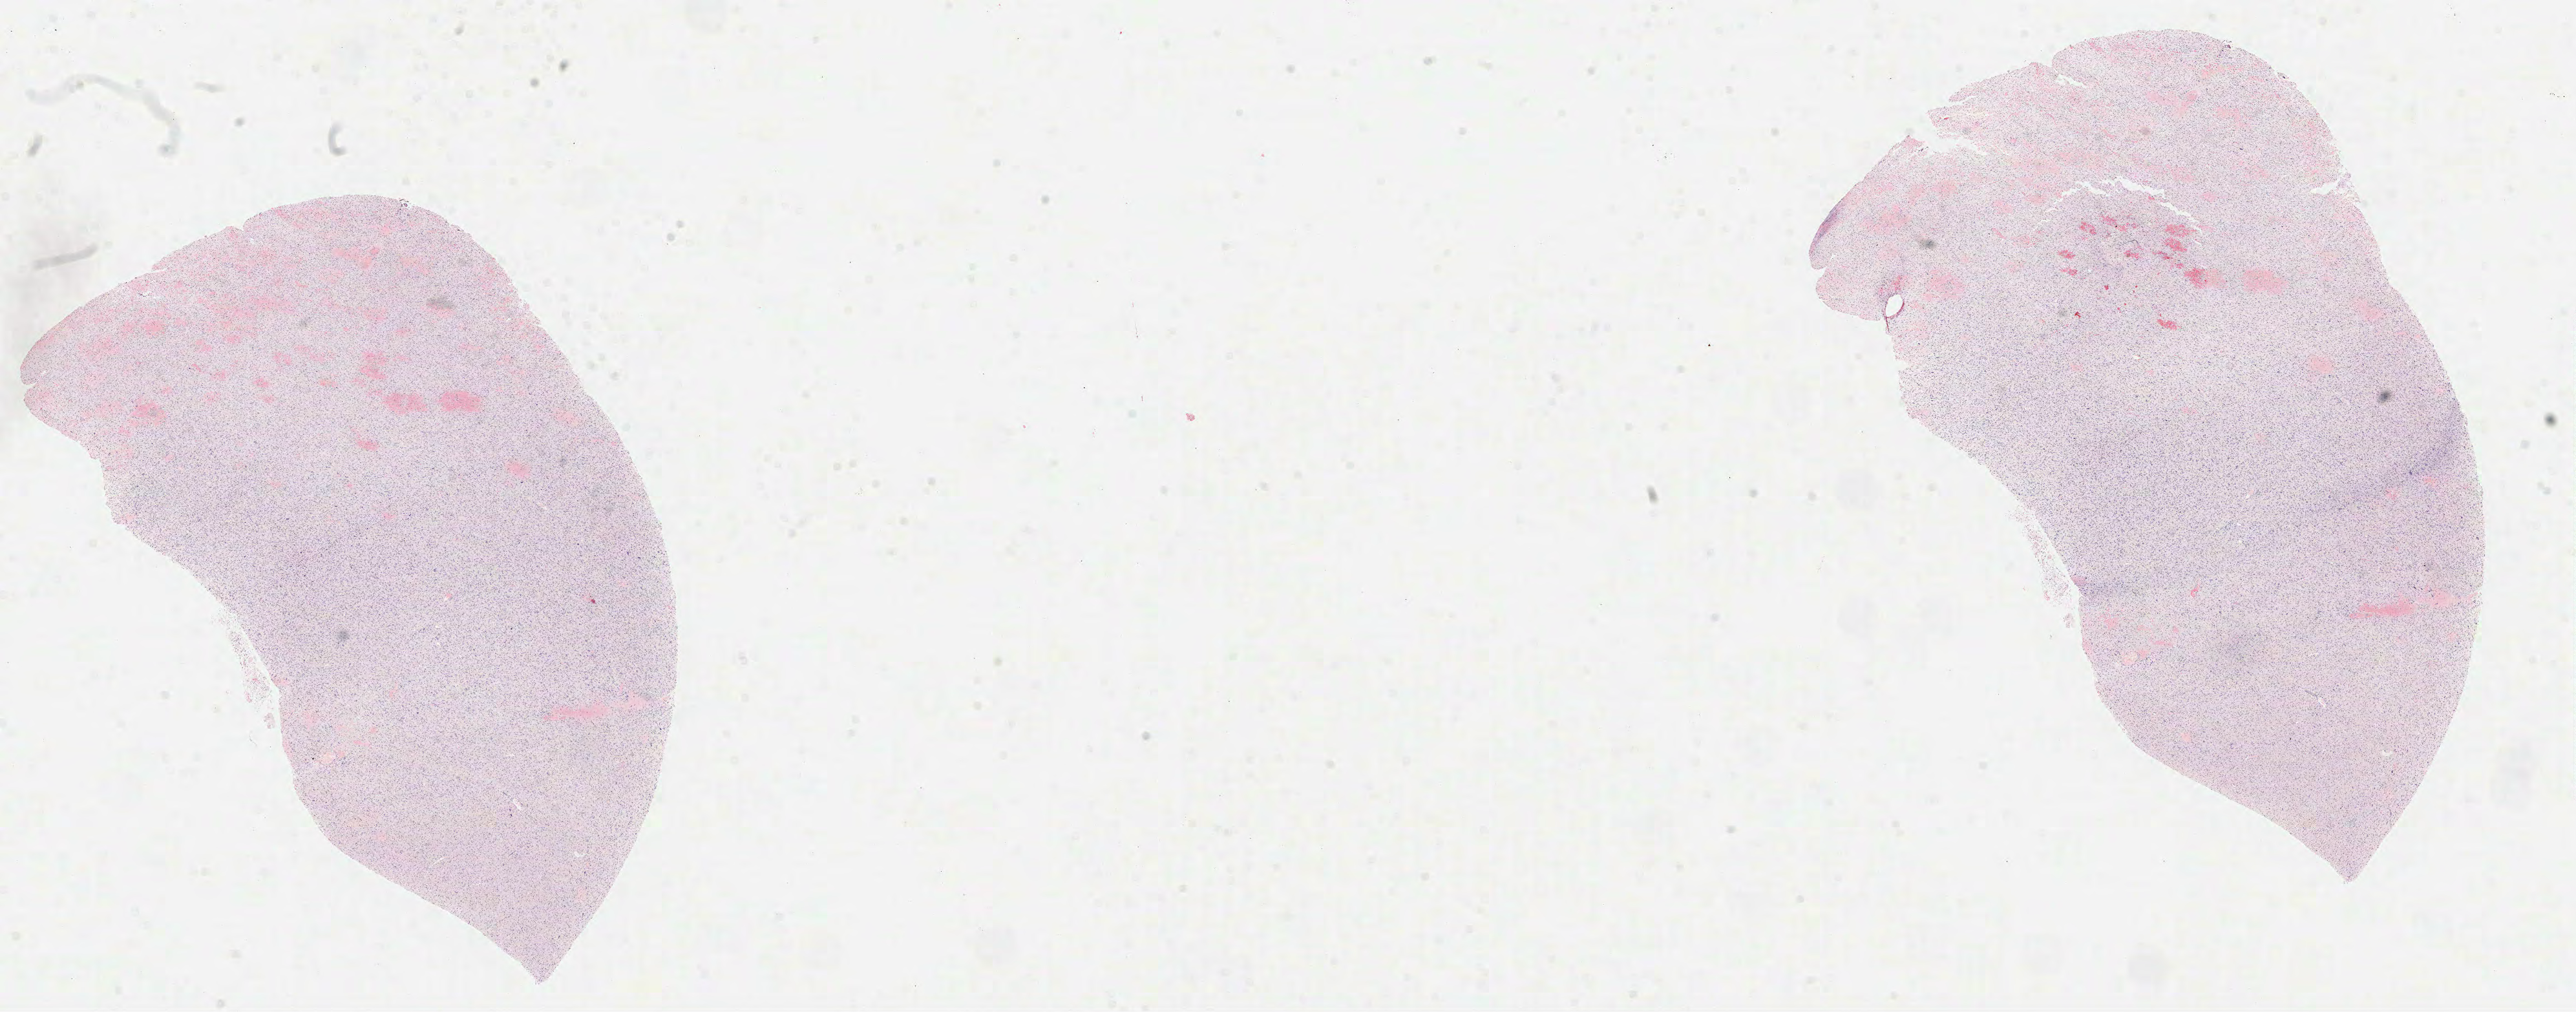
Hematoxylin and eosin (H&E) stained whole-slide image — a low-resolution overview of the entire scanned area, about 32.1 x 12.6 mm (acquisition: 40x scan), formalin-fixed paraffin-embedded (FFPE) diagnostic section, sample: primary tumour, brain. Female patient; age at initial diagnosis 76 years.
Diagnosis: Glioblastoma.